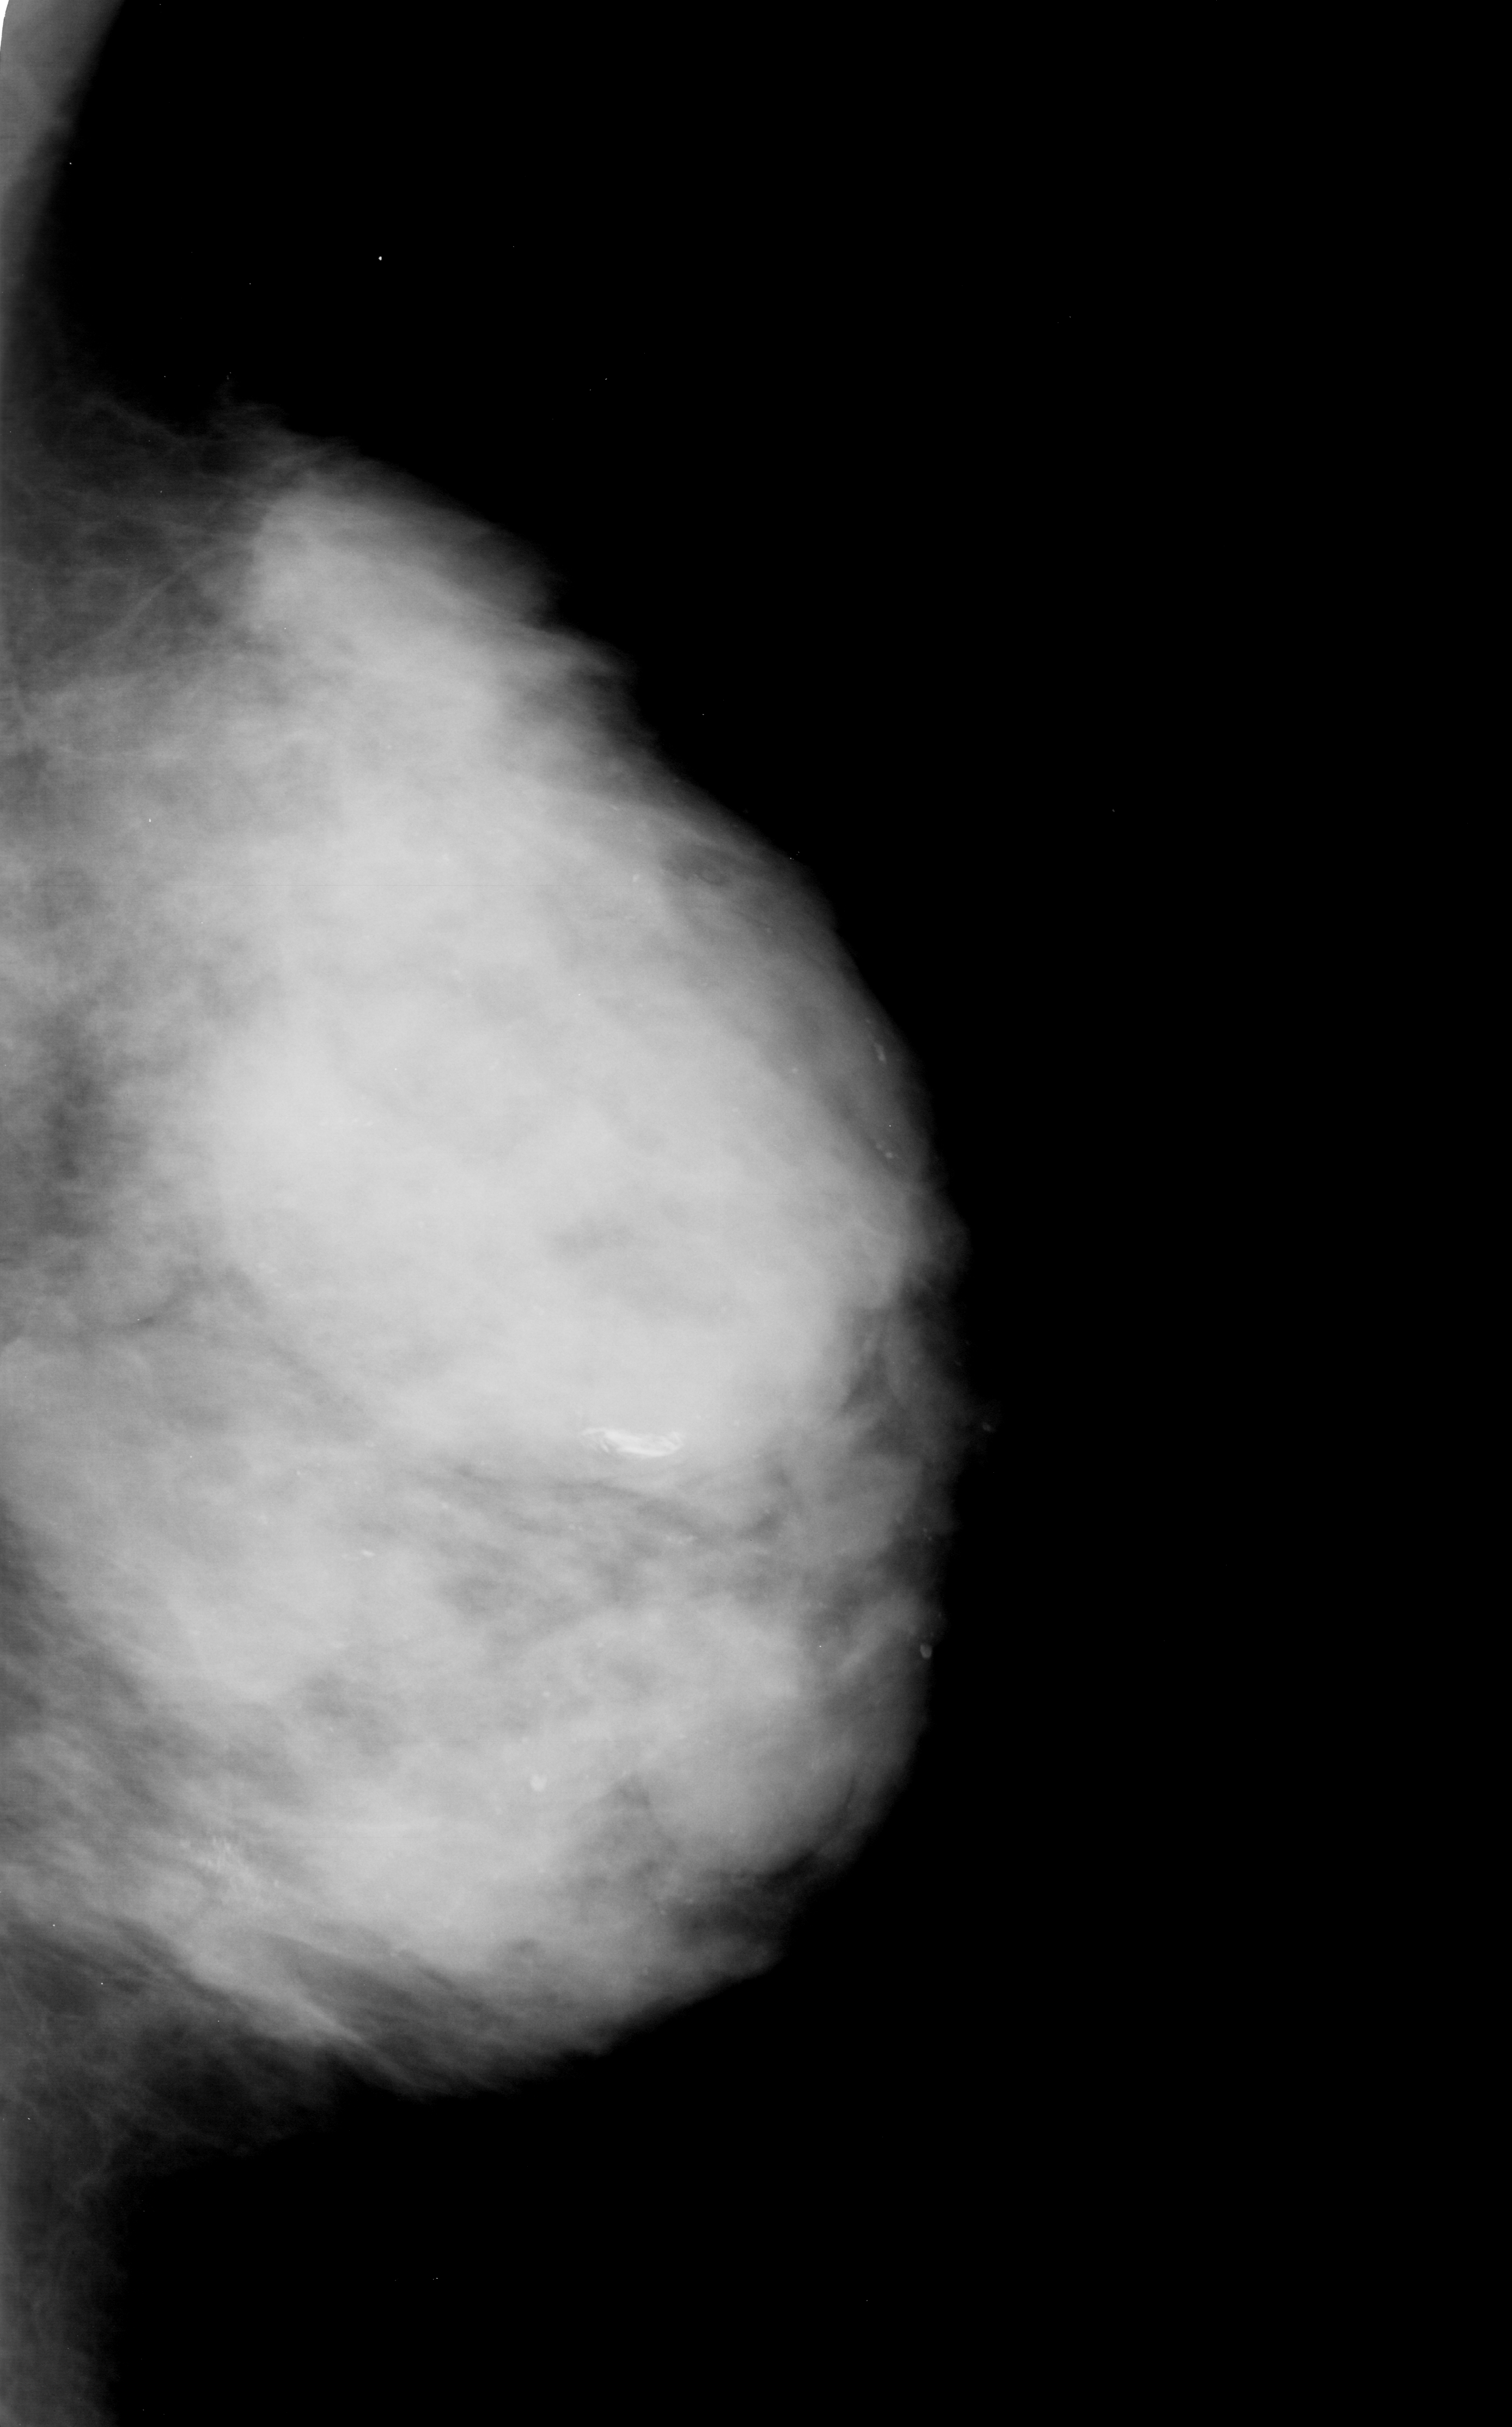
Digitized screen-film mammogram, left breast, mediolateral oblique (MLO) view.
Calcifications, morphology pleomorphic, distribution clustered; BI-RADS assessment category 3; pathology result (as recorded, not read from the image): malignant.